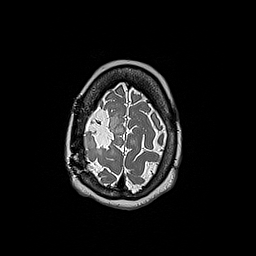
Brain MRI from a brain-tumour surgery series, one axial slice. Slice 45 of 192 in the series (ordered by position). 256 × 256 image matrix, field of view 250 × 250 mm. From the clinical record (not read from this slice): histopathology: Oligodendroglioma; WHO grade: 3; IDH mutation: yes; tumour location: Right Frontal.
Outlined on this slice (manually delineated by an expert):
- tumour: box from (x=84, y=132) to (x=98, y=151) px